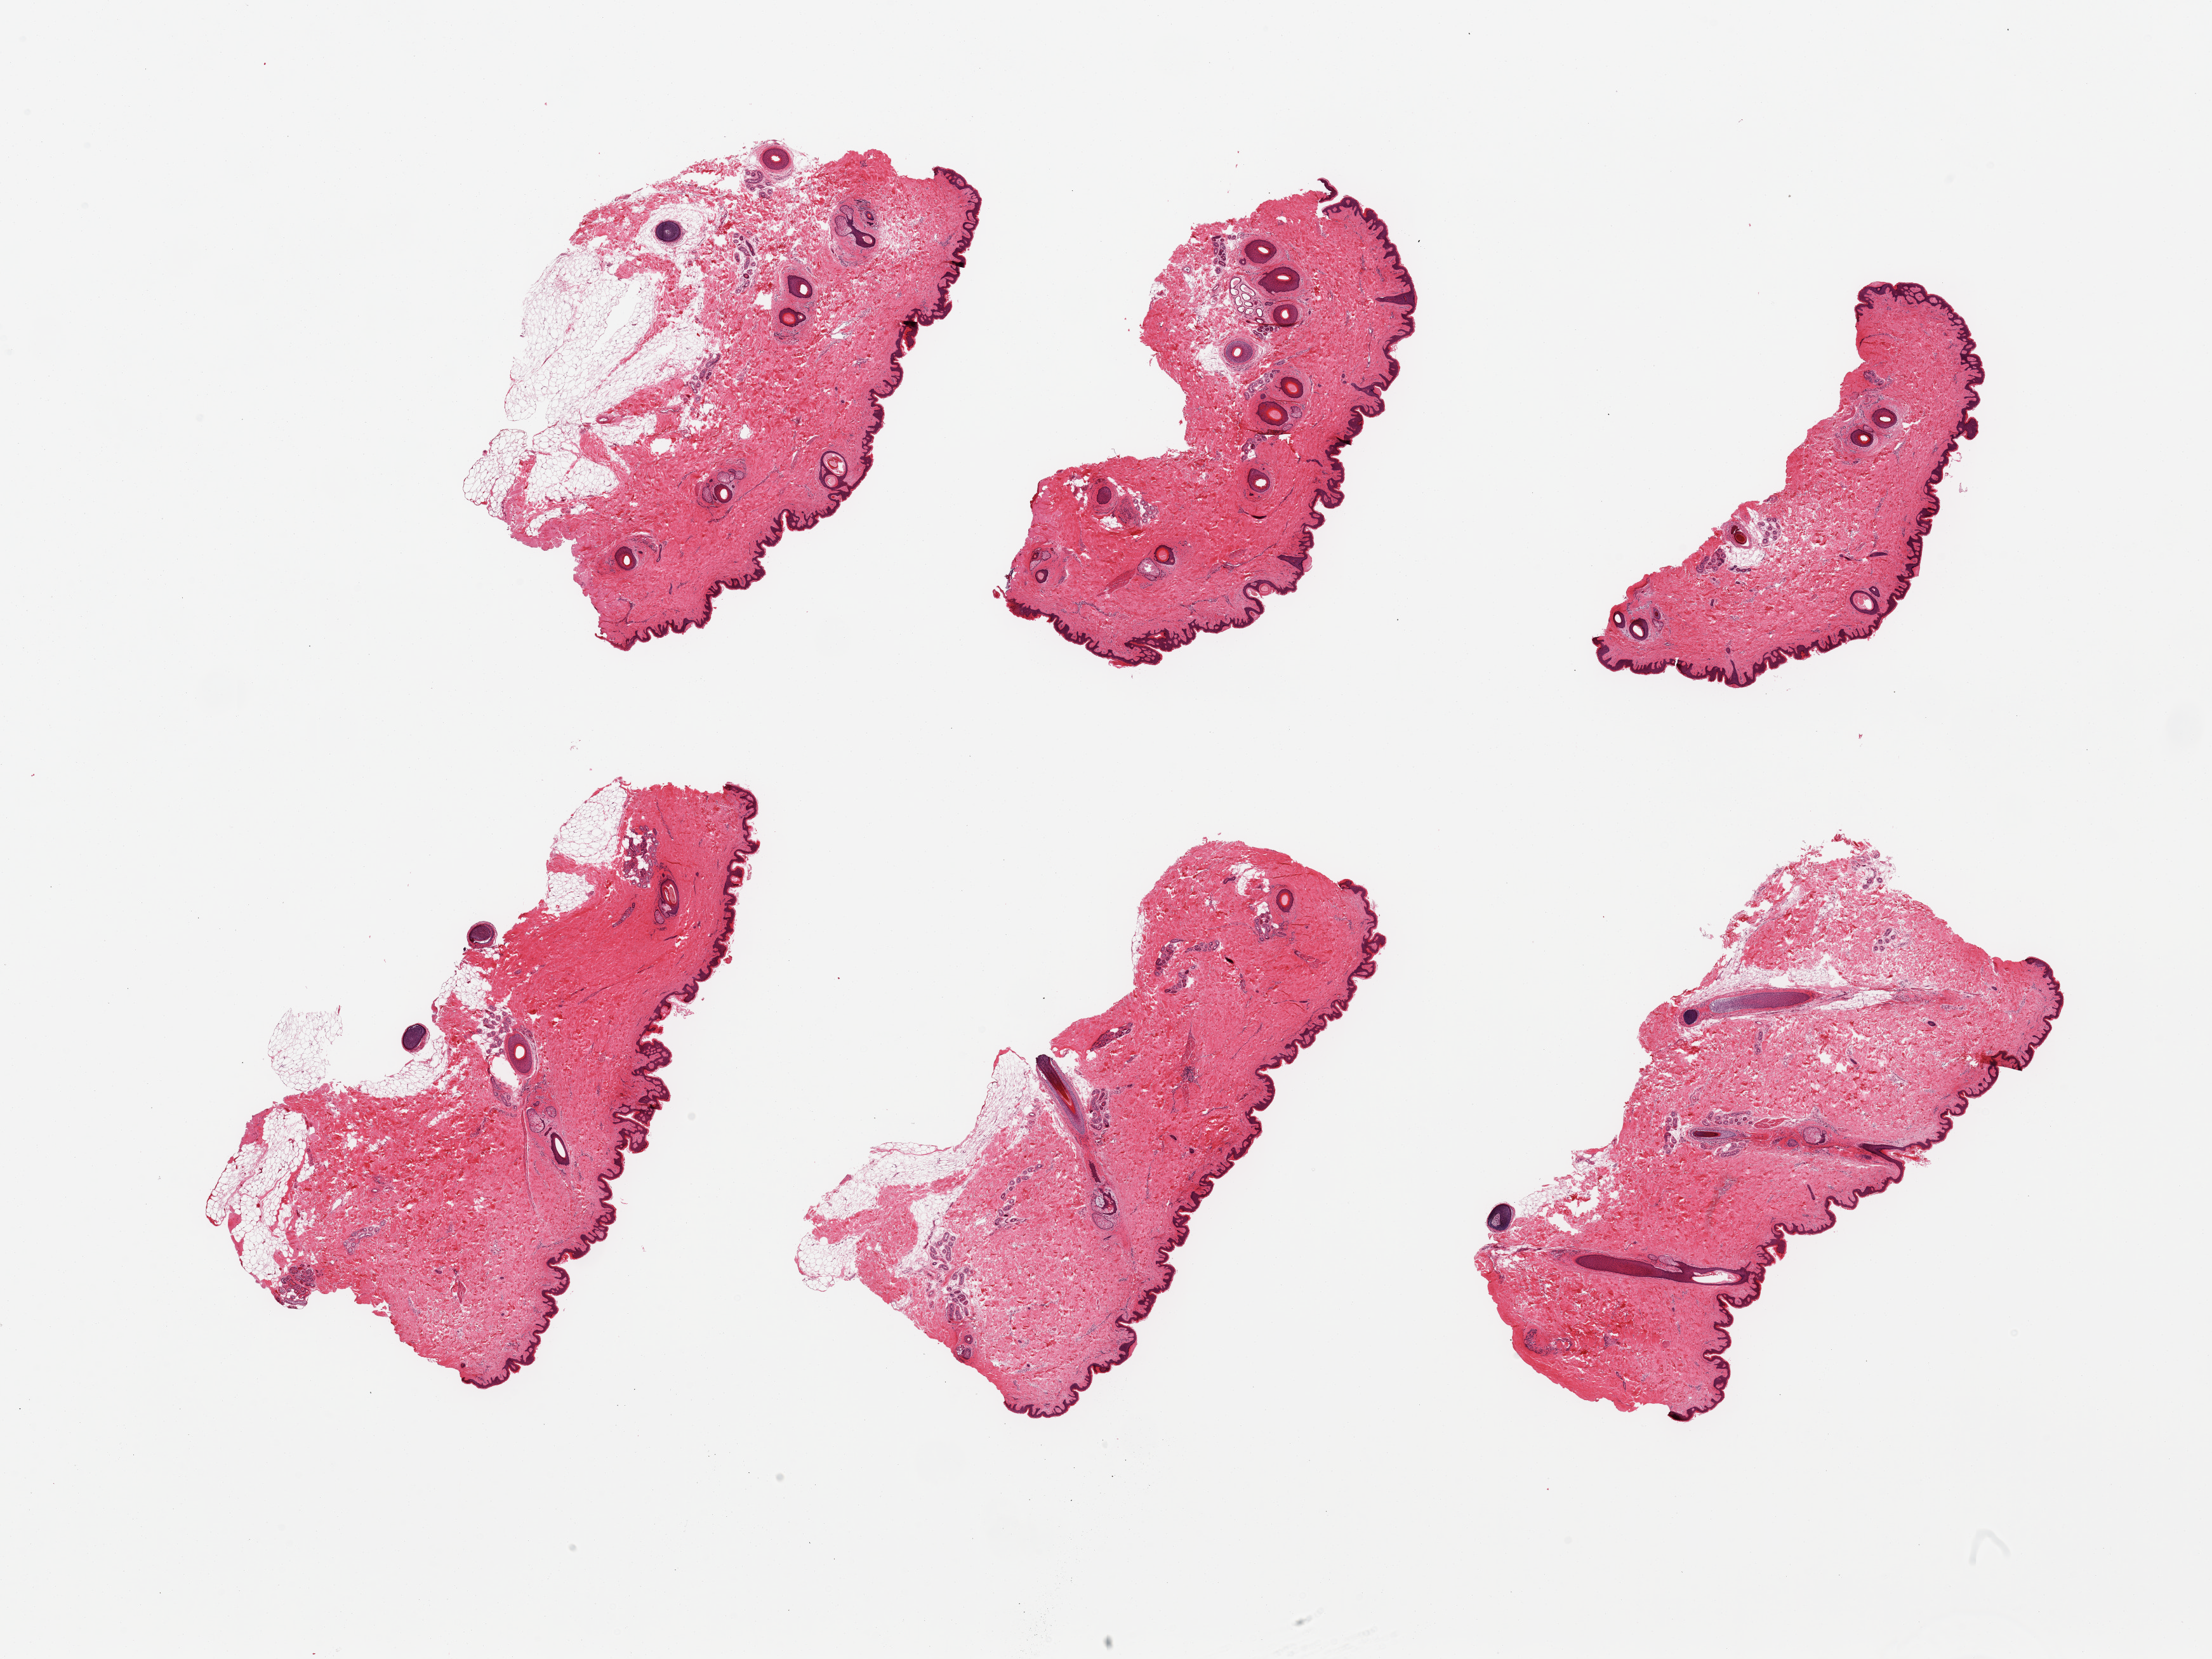
Digitized H&E-stained section — a low-resolution overview of the entire scanned area, about 27.6 x 20.7 mm, PAXgene-fixed paraffin-embedded (PFPE) section, section of skin of suprapubic region (target tissue), donor tissue sample.
Pathologist's review note for this sample: 6 pieces; up to 10 hair follicles per piece; 3 pieces have subcutaneous fat up to 1.5mm thick; dermal fat <10%.